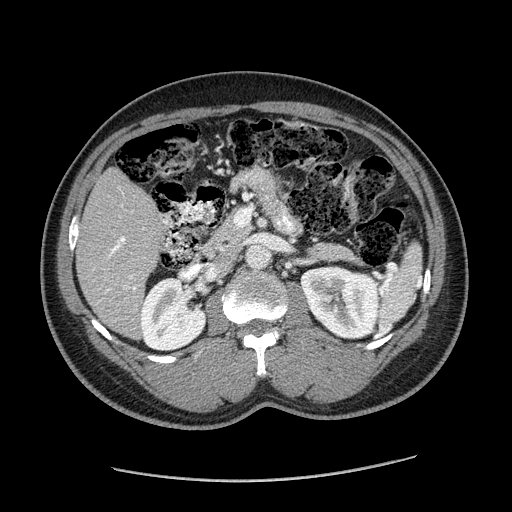
Contrast-enhanced abdominal CT (liver protocol), one axial slice; reconstruction kernel STANDARD; soft-tissue window (W 400 / L 40 HU); 2.5 mm slice thickness; 512 × 512 image matrix, field of view 400 × 400 mm. Case-level facts recorded for this patient, not image findings: diagnosis: hepatocellular carcinoma (patient treated with transarterial chemoembolisation; whether this scan precedes or follows treatment is not stated here); TNM stage (as recorded): Stage-I; Child-Pugh class: A; tumour nodularity: uninodular; tumour size: 3.1 cm.
Annotated regions visible in this slice (semi-automatically segmented with operator editing):
- liver parenchyma outside the tumour (the mass and vessels are separate outlines, so this box may not span the whole liver): box from (x=76, y=168) to (x=166, y=336) px
- liver vessels: (x=107, y=236)–(x=136, y=291)